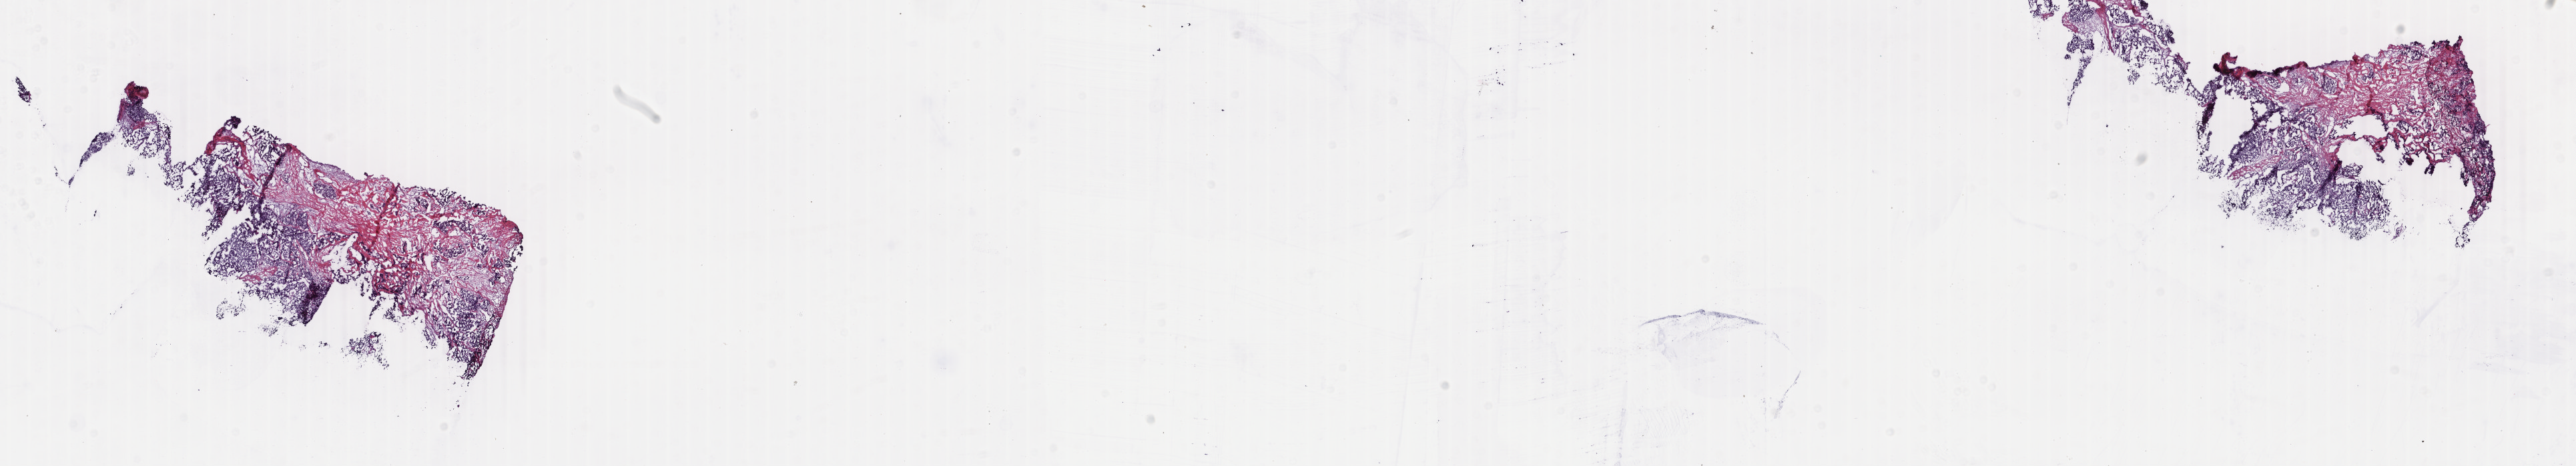
Digitized H&E-stained tissue section (whole slide) — a low-resolution overview of the entire scanned area, about 30.7 x 5.6 mm (from a 40x scan); frozen section from the bottom of the tissue portion; breast, primary tumour sample. Female patient; age at initial diagnosis 54 years. Pathologist review of this section (percent, as recorded): tumour cells 65%, tumour nuclei 90%, normal cells 0%, stromal cells 33%, necrosis 2%. Inflammatory infiltration, as recorded: lymphocyte infiltration 3%, monocyte infiltration 1%, neutrophil infiltration 0%.
• diagnosis: Infiltrating duct carcinoma, NOS
• lymph nodes positive (case pathology): 0 of 26 examined
• AJCC pathologic stage: IIB (6th edition)
• laterality: right